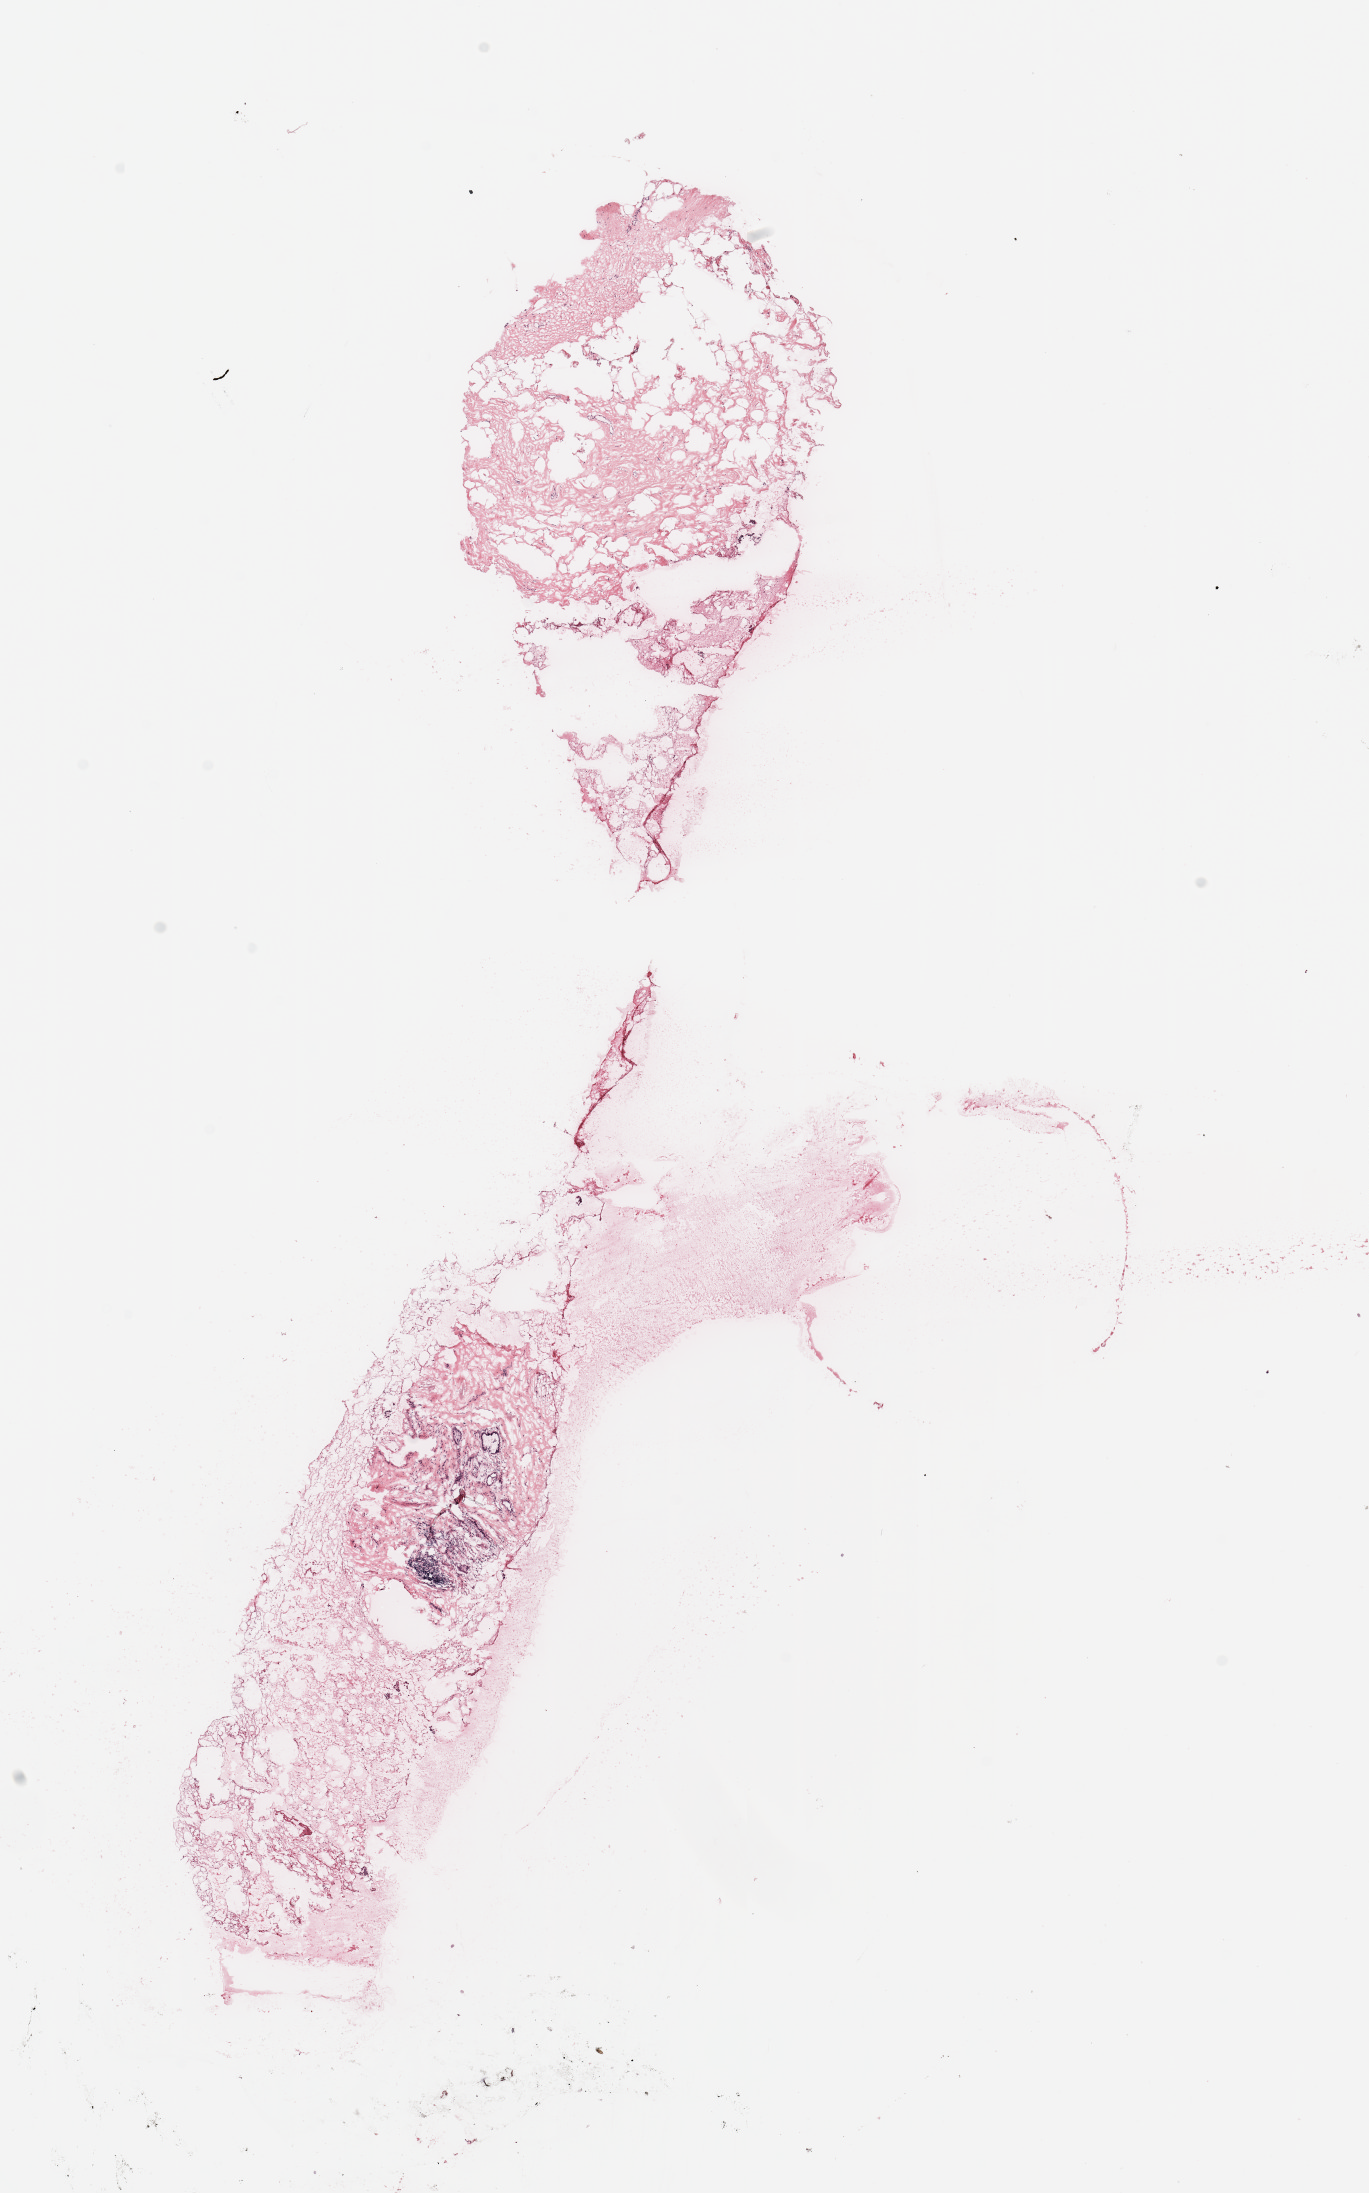
H&E whole-slide image — a low-resolution overview of the entire scanned area, about 10.8 x 17.3 mm. Breast, tissue type not recorded.
Patient diagnosis (cohort enrolment): breast cancer (breast).